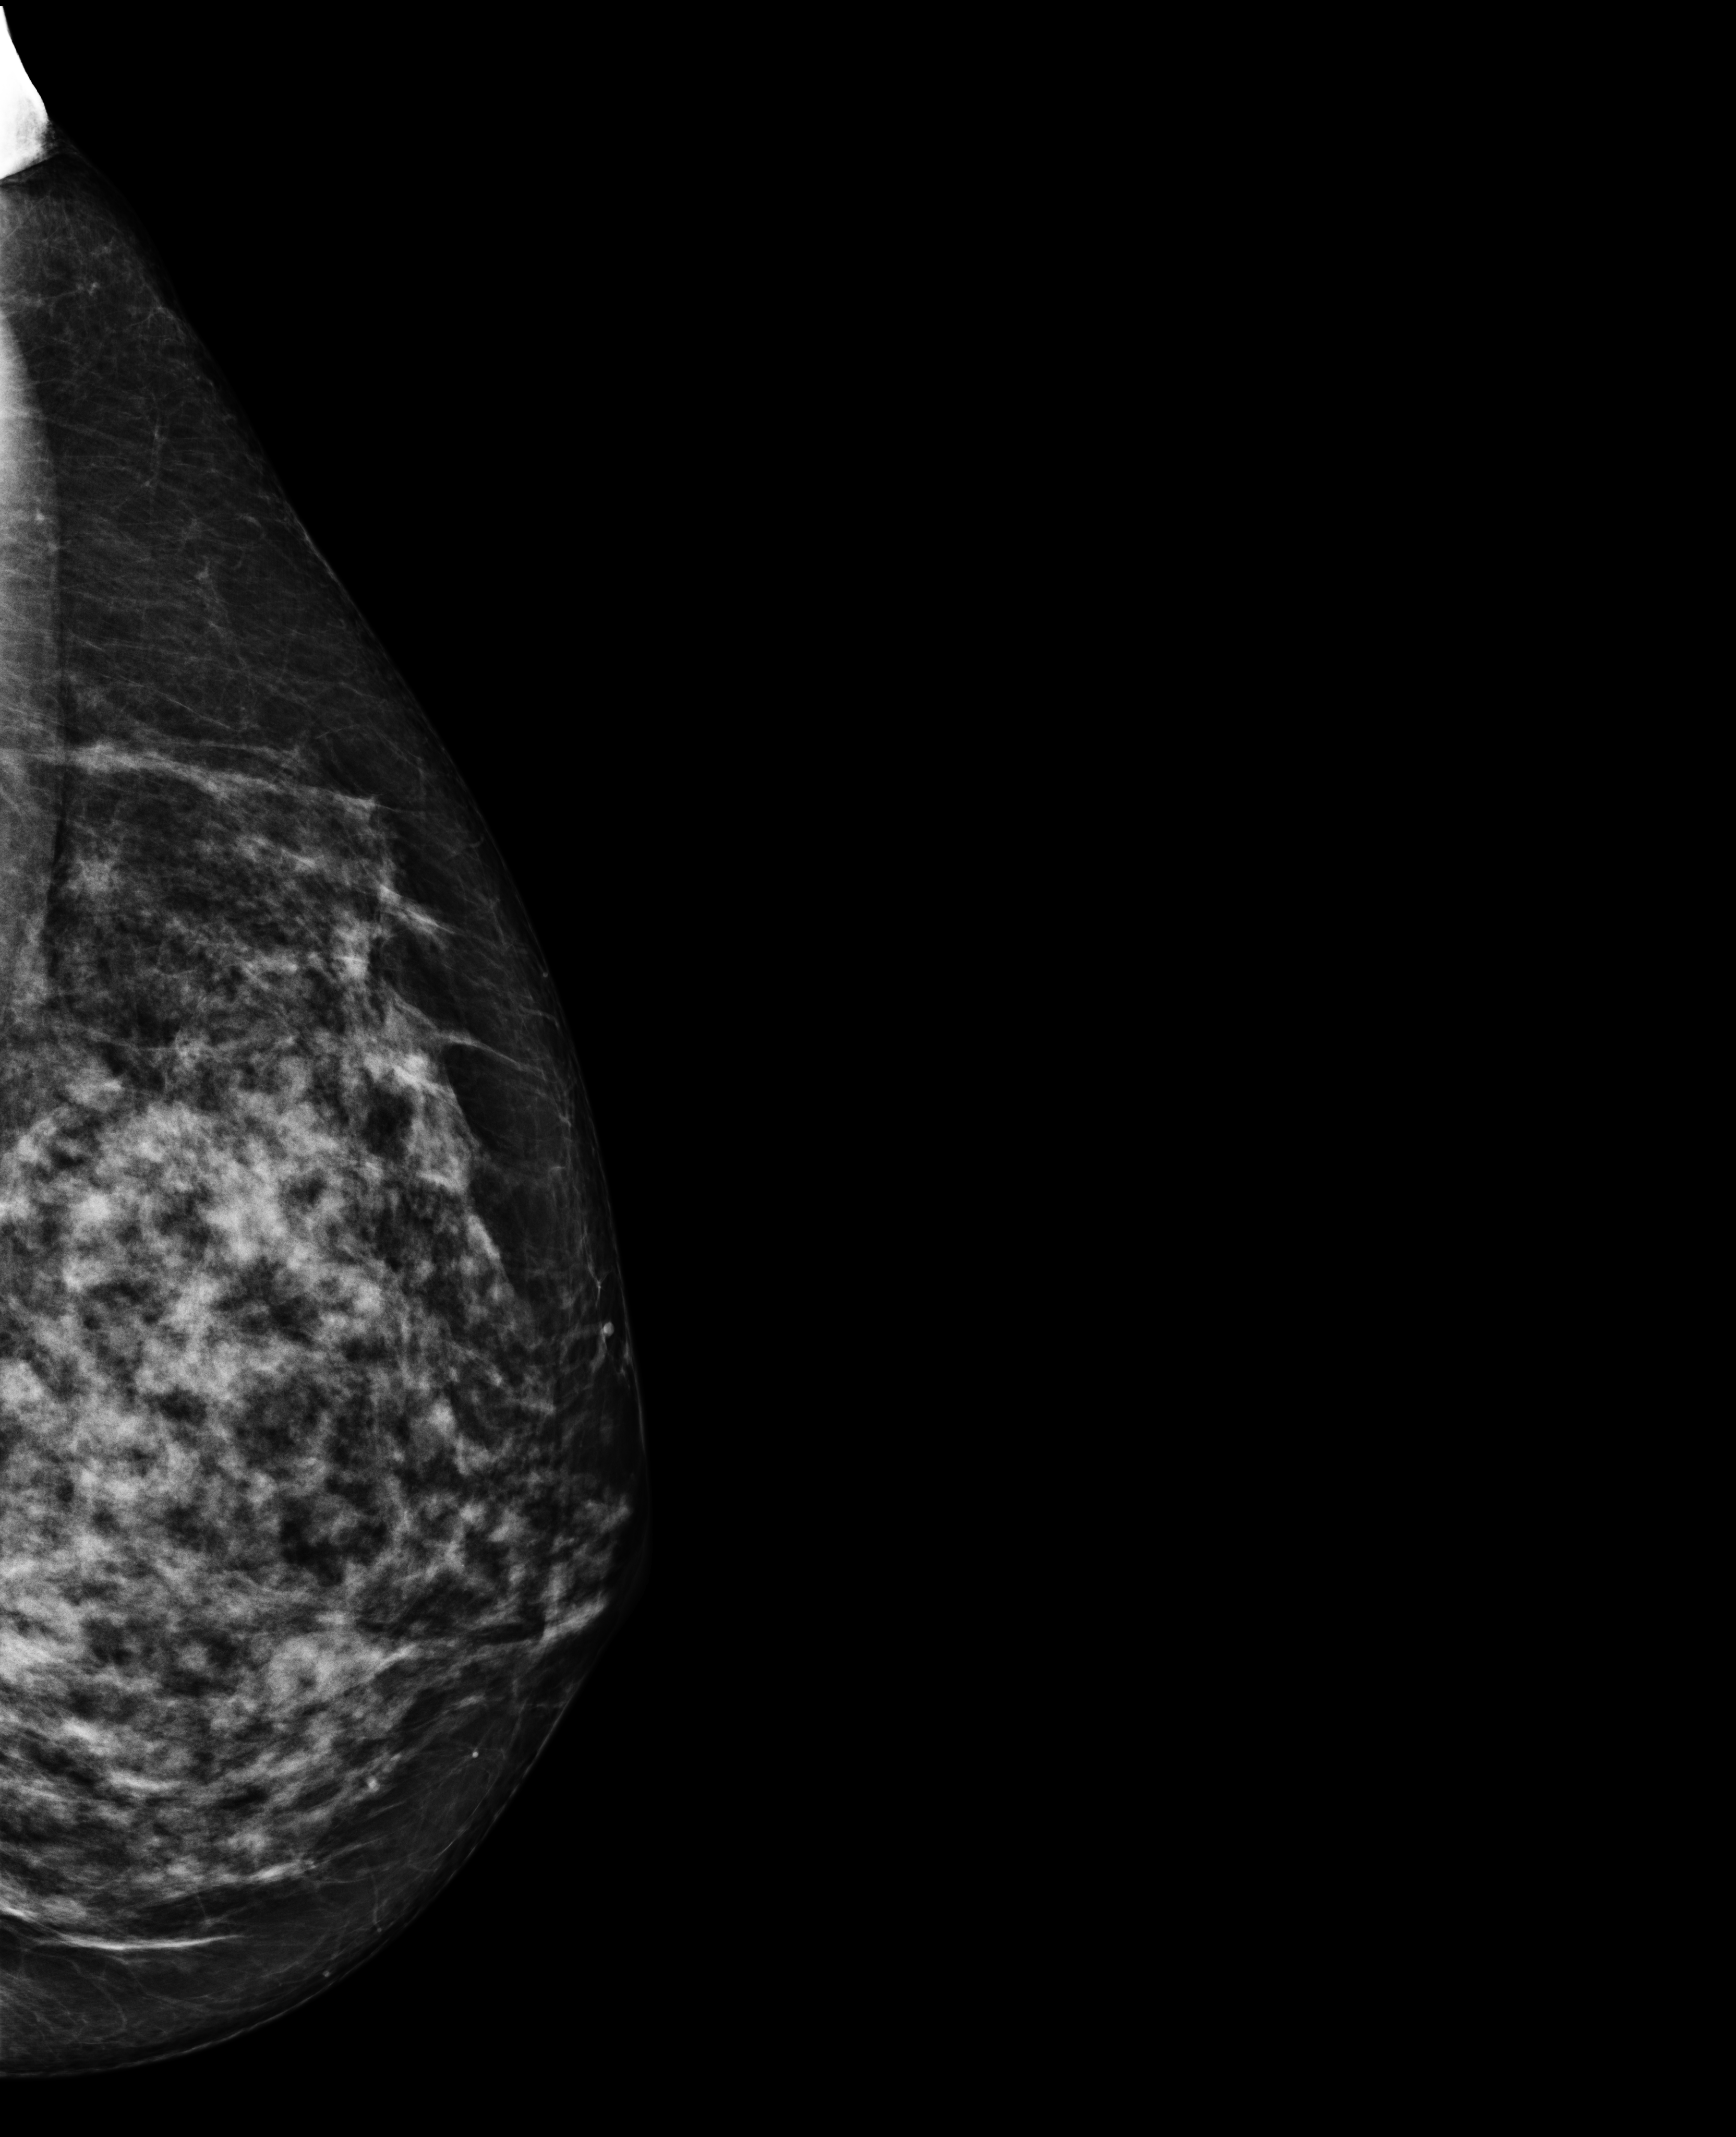
Digital mammogram (FFDM); left breast; exaggerated CC view (lateral) (axillary tissue); screening examination; system: Selenia Dimensions. Patient: female, 43 years.
BI-RADS breast density category at the screening exam (both breasts, scale 1–4): 4. Final BI-RADS category for the screening round (tomosynthesis exam, both breasts): category 2. Recall: recalled for additional imaging after this screen.